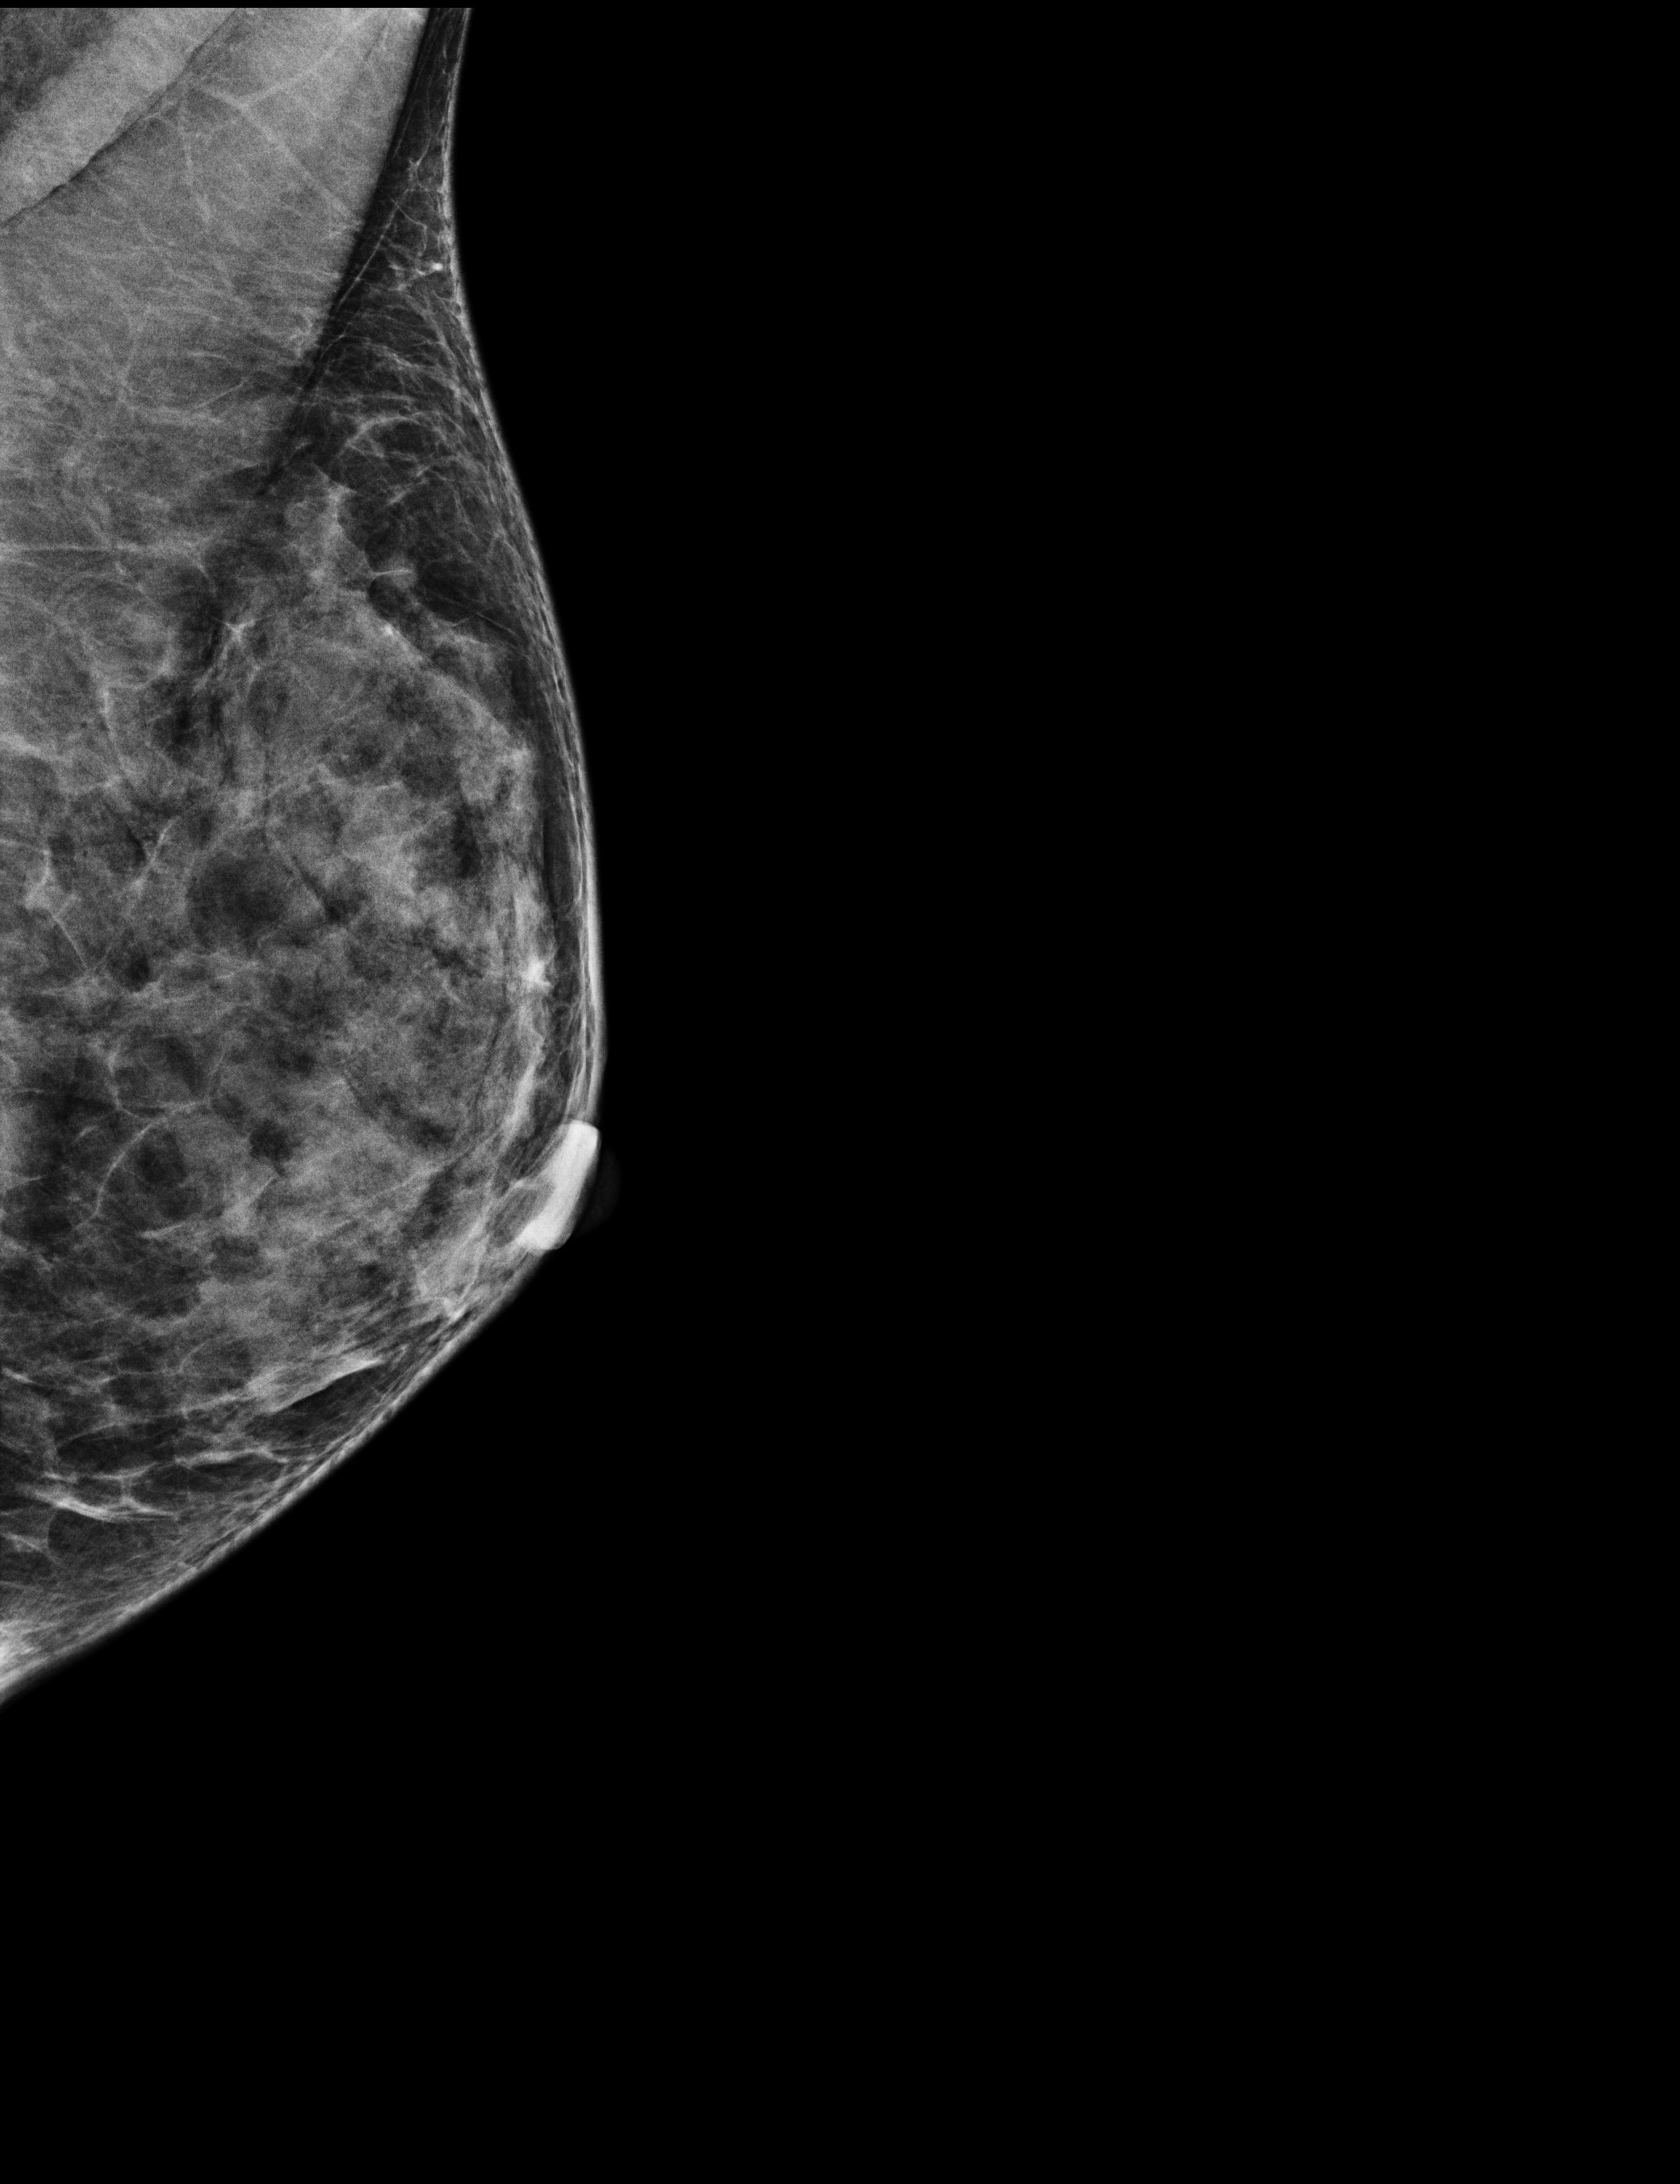
Screening examination. Patient aged 44 years (female).
Image type: full-field digital mammogram. Breast: left. Projection: mediolateral oblique (MLO) view.